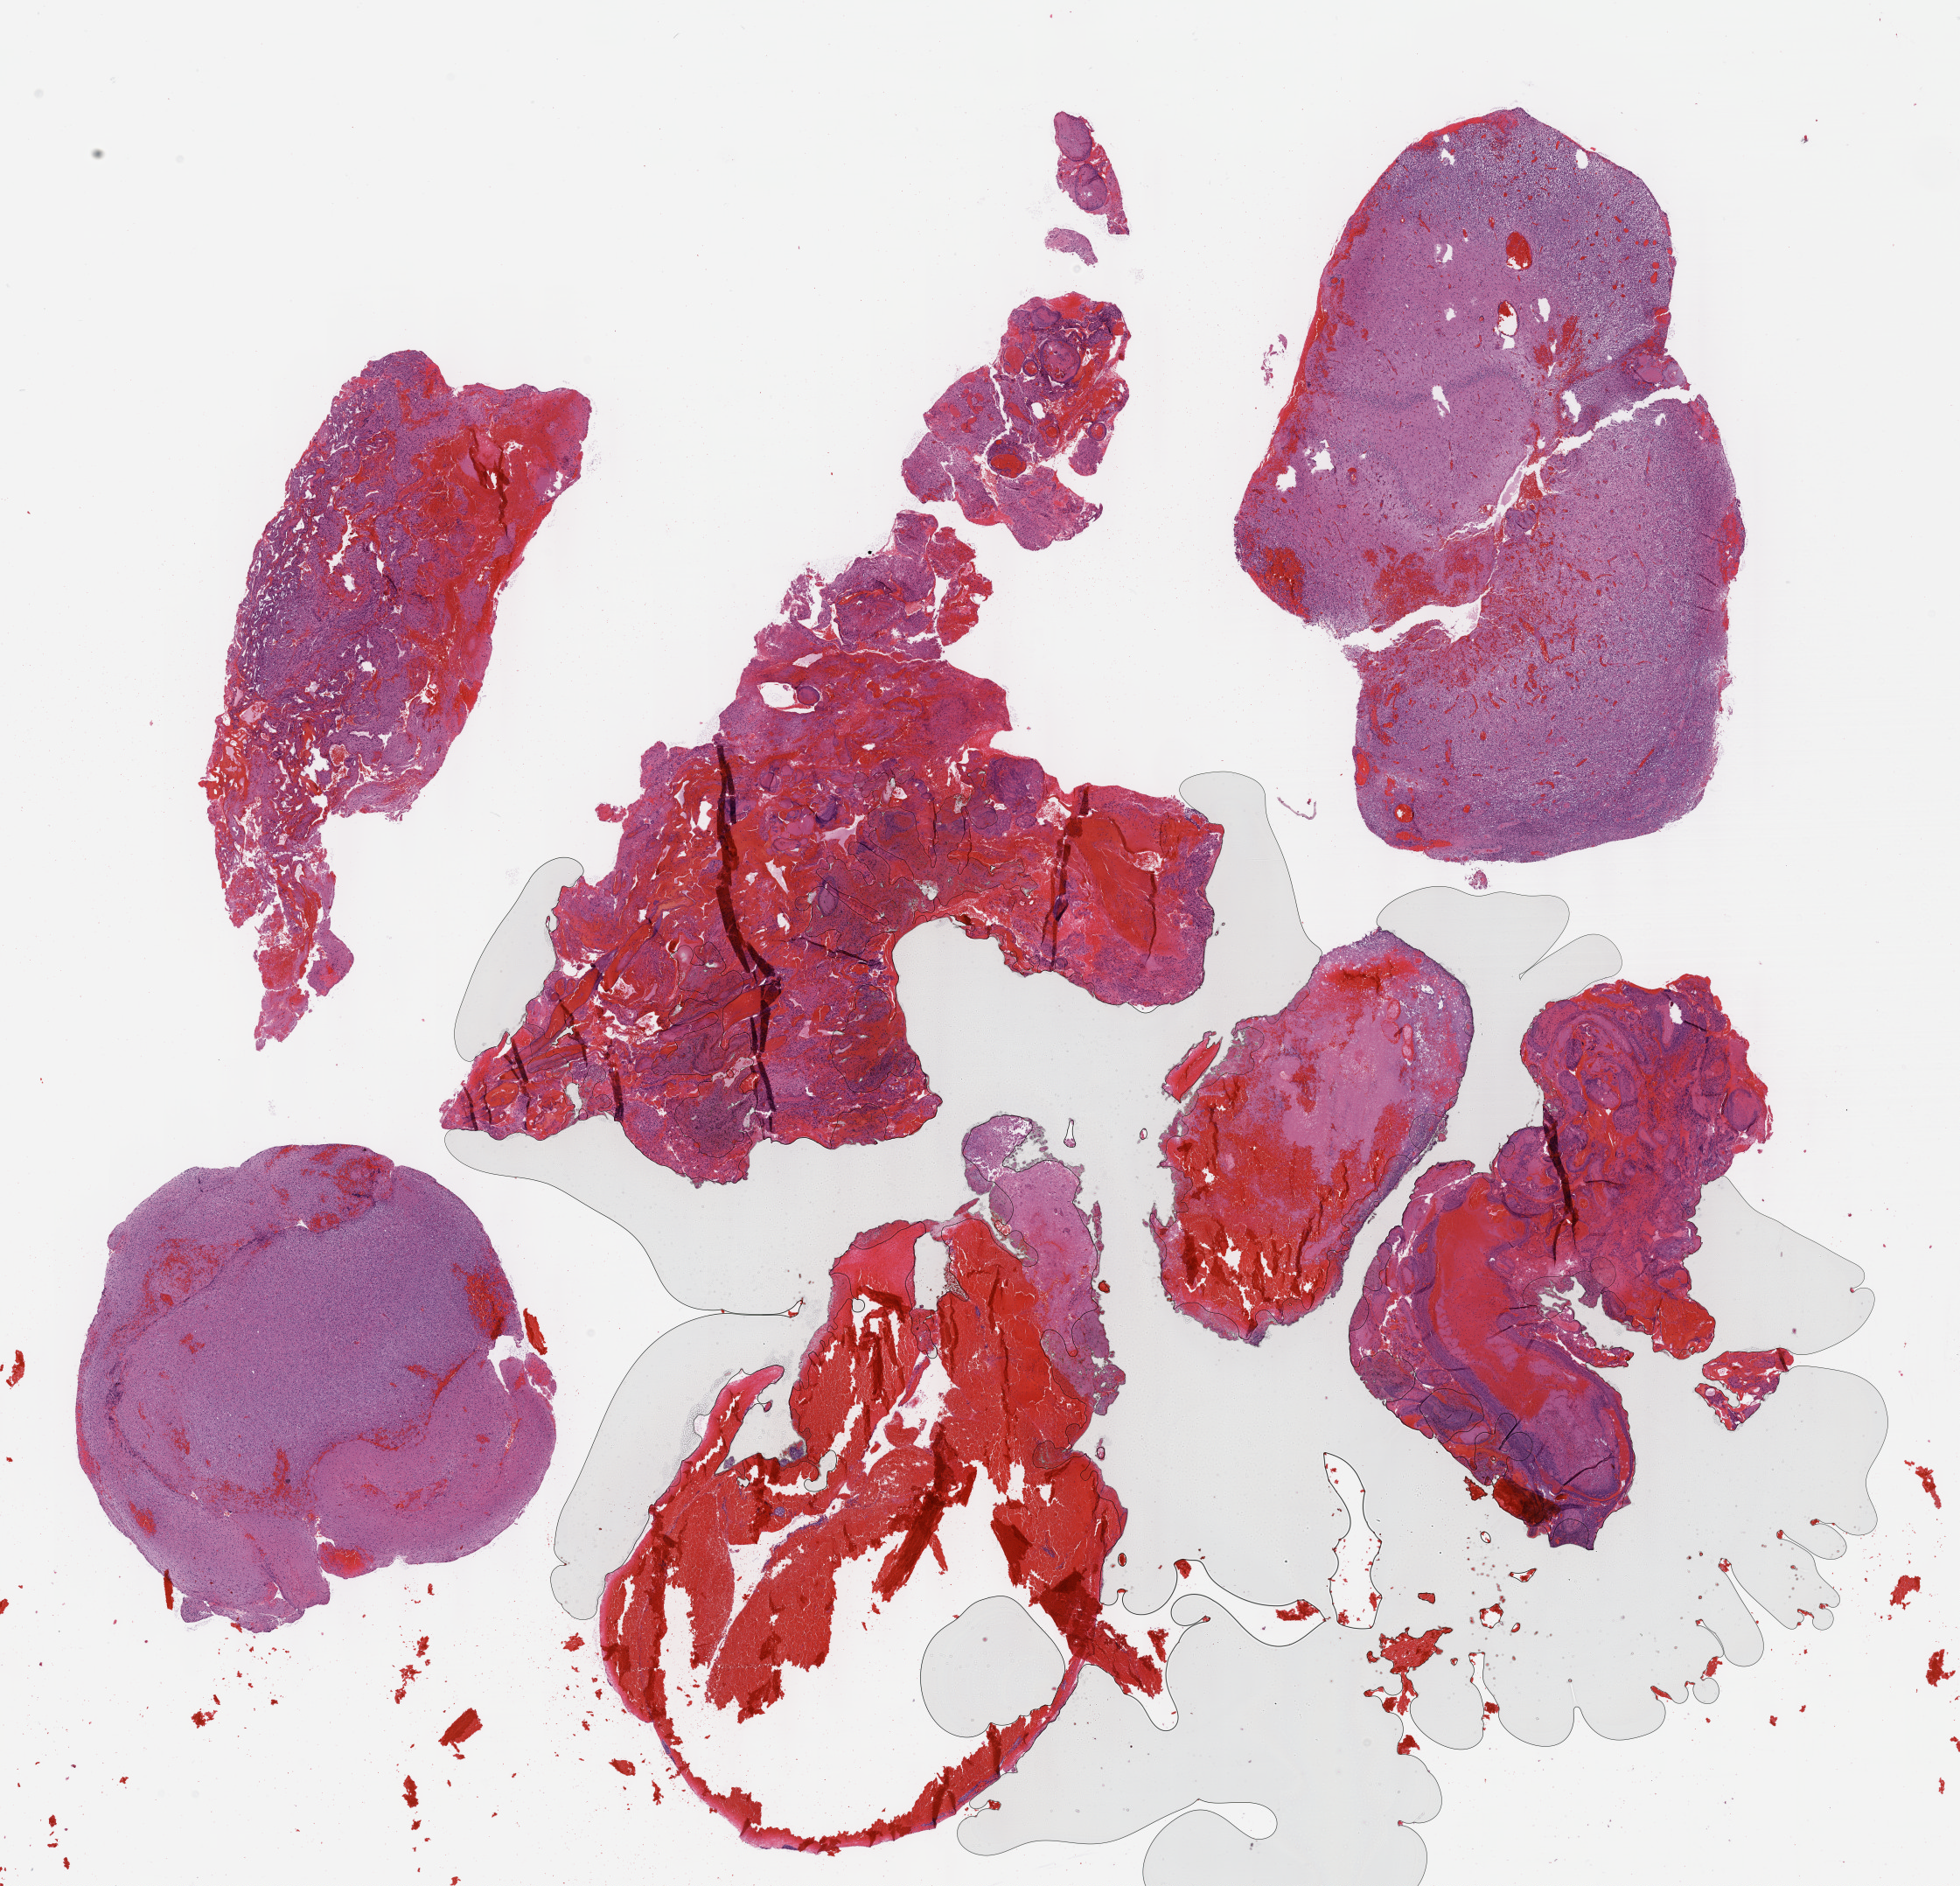
Whole-slide histology image, H&E-stained, shown as a low-resolution overview of the whole scanned area (about 18.1 x 17.4 mm, from a 40x scan). Formalin-fixed paraffin-embedded (FFPE) diagnostic section. Sample: primary tumour, brain. Male patient; age at initial diagnosis 66 years. Histologic grade: G3 (poorly differentiated).
- histologic diagnosis: Oligodendroglioma, anaplastic (cerebrum)